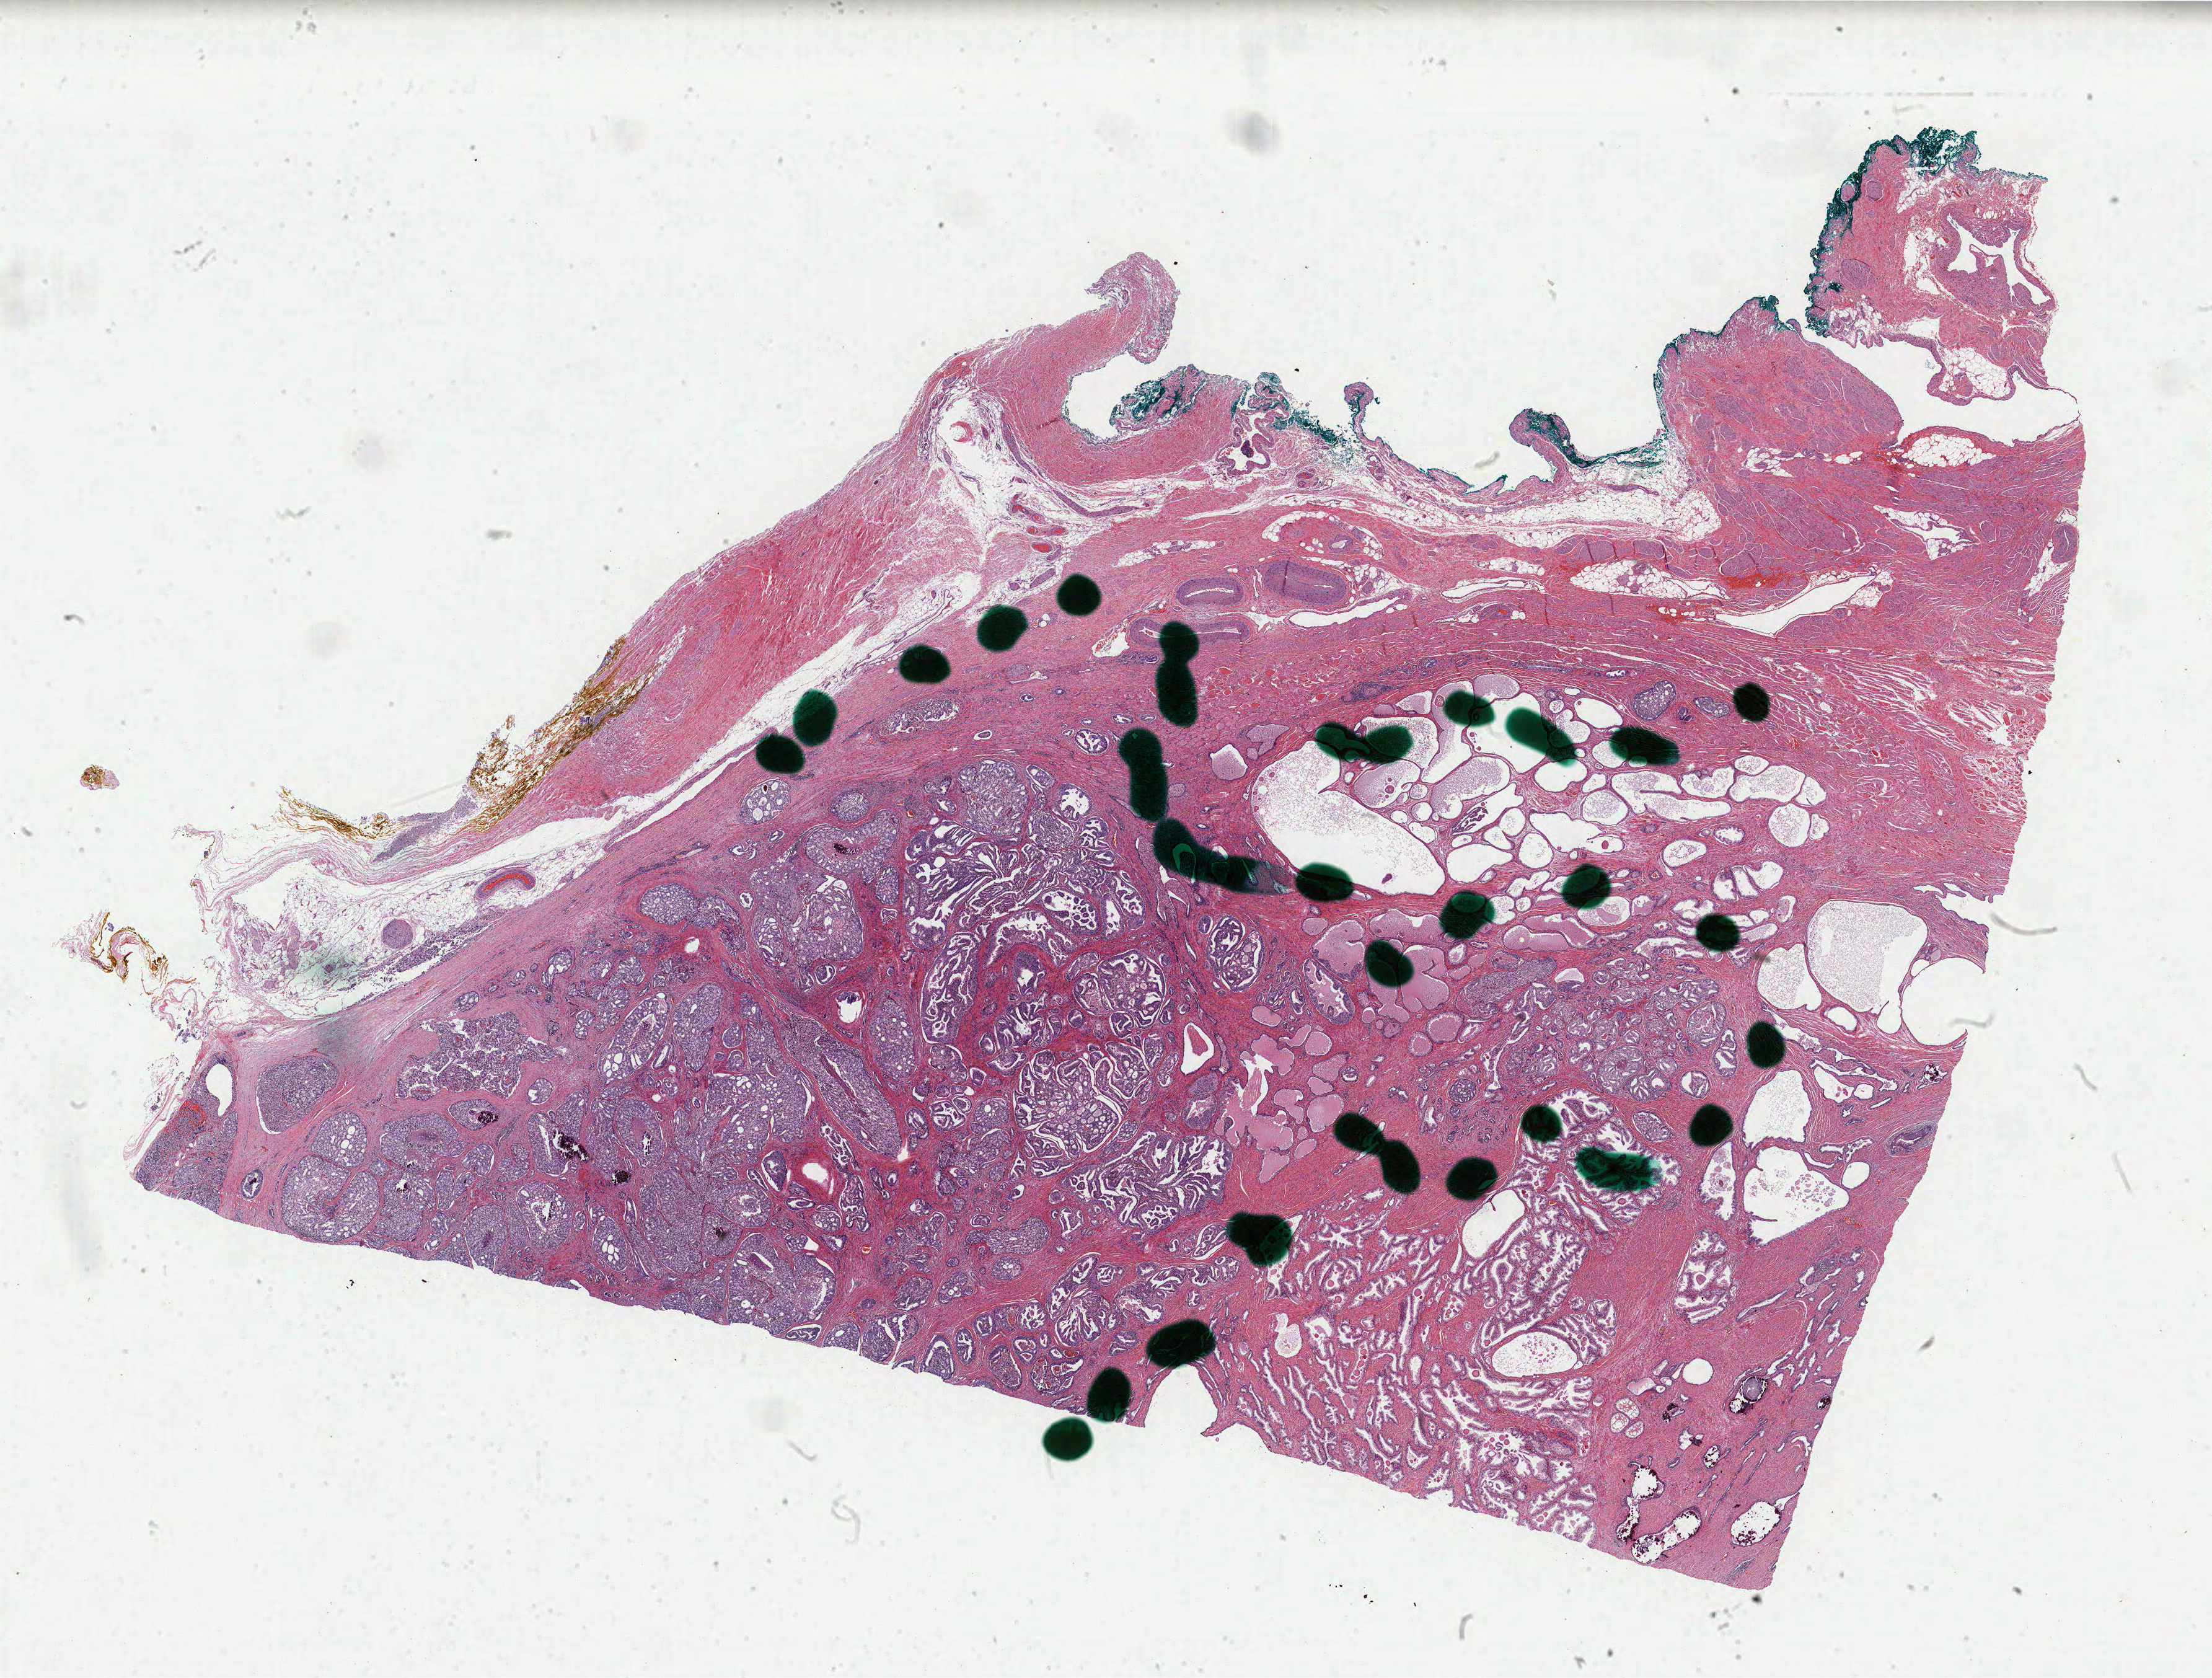
H&E-stained whole-slide image — shown as a low-resolution overview of the whole scanned area (about 28.3 x 21.5 mm); FFPE section; sample: primary tumour, prostate. Patient: male, age at initial diagnosis 62 years. Gleason score: 9 (4+5).
* diagnosis: Adenocarcinoma, NOS
* lymph nodes positive (case pathology): 0 of 17 examined